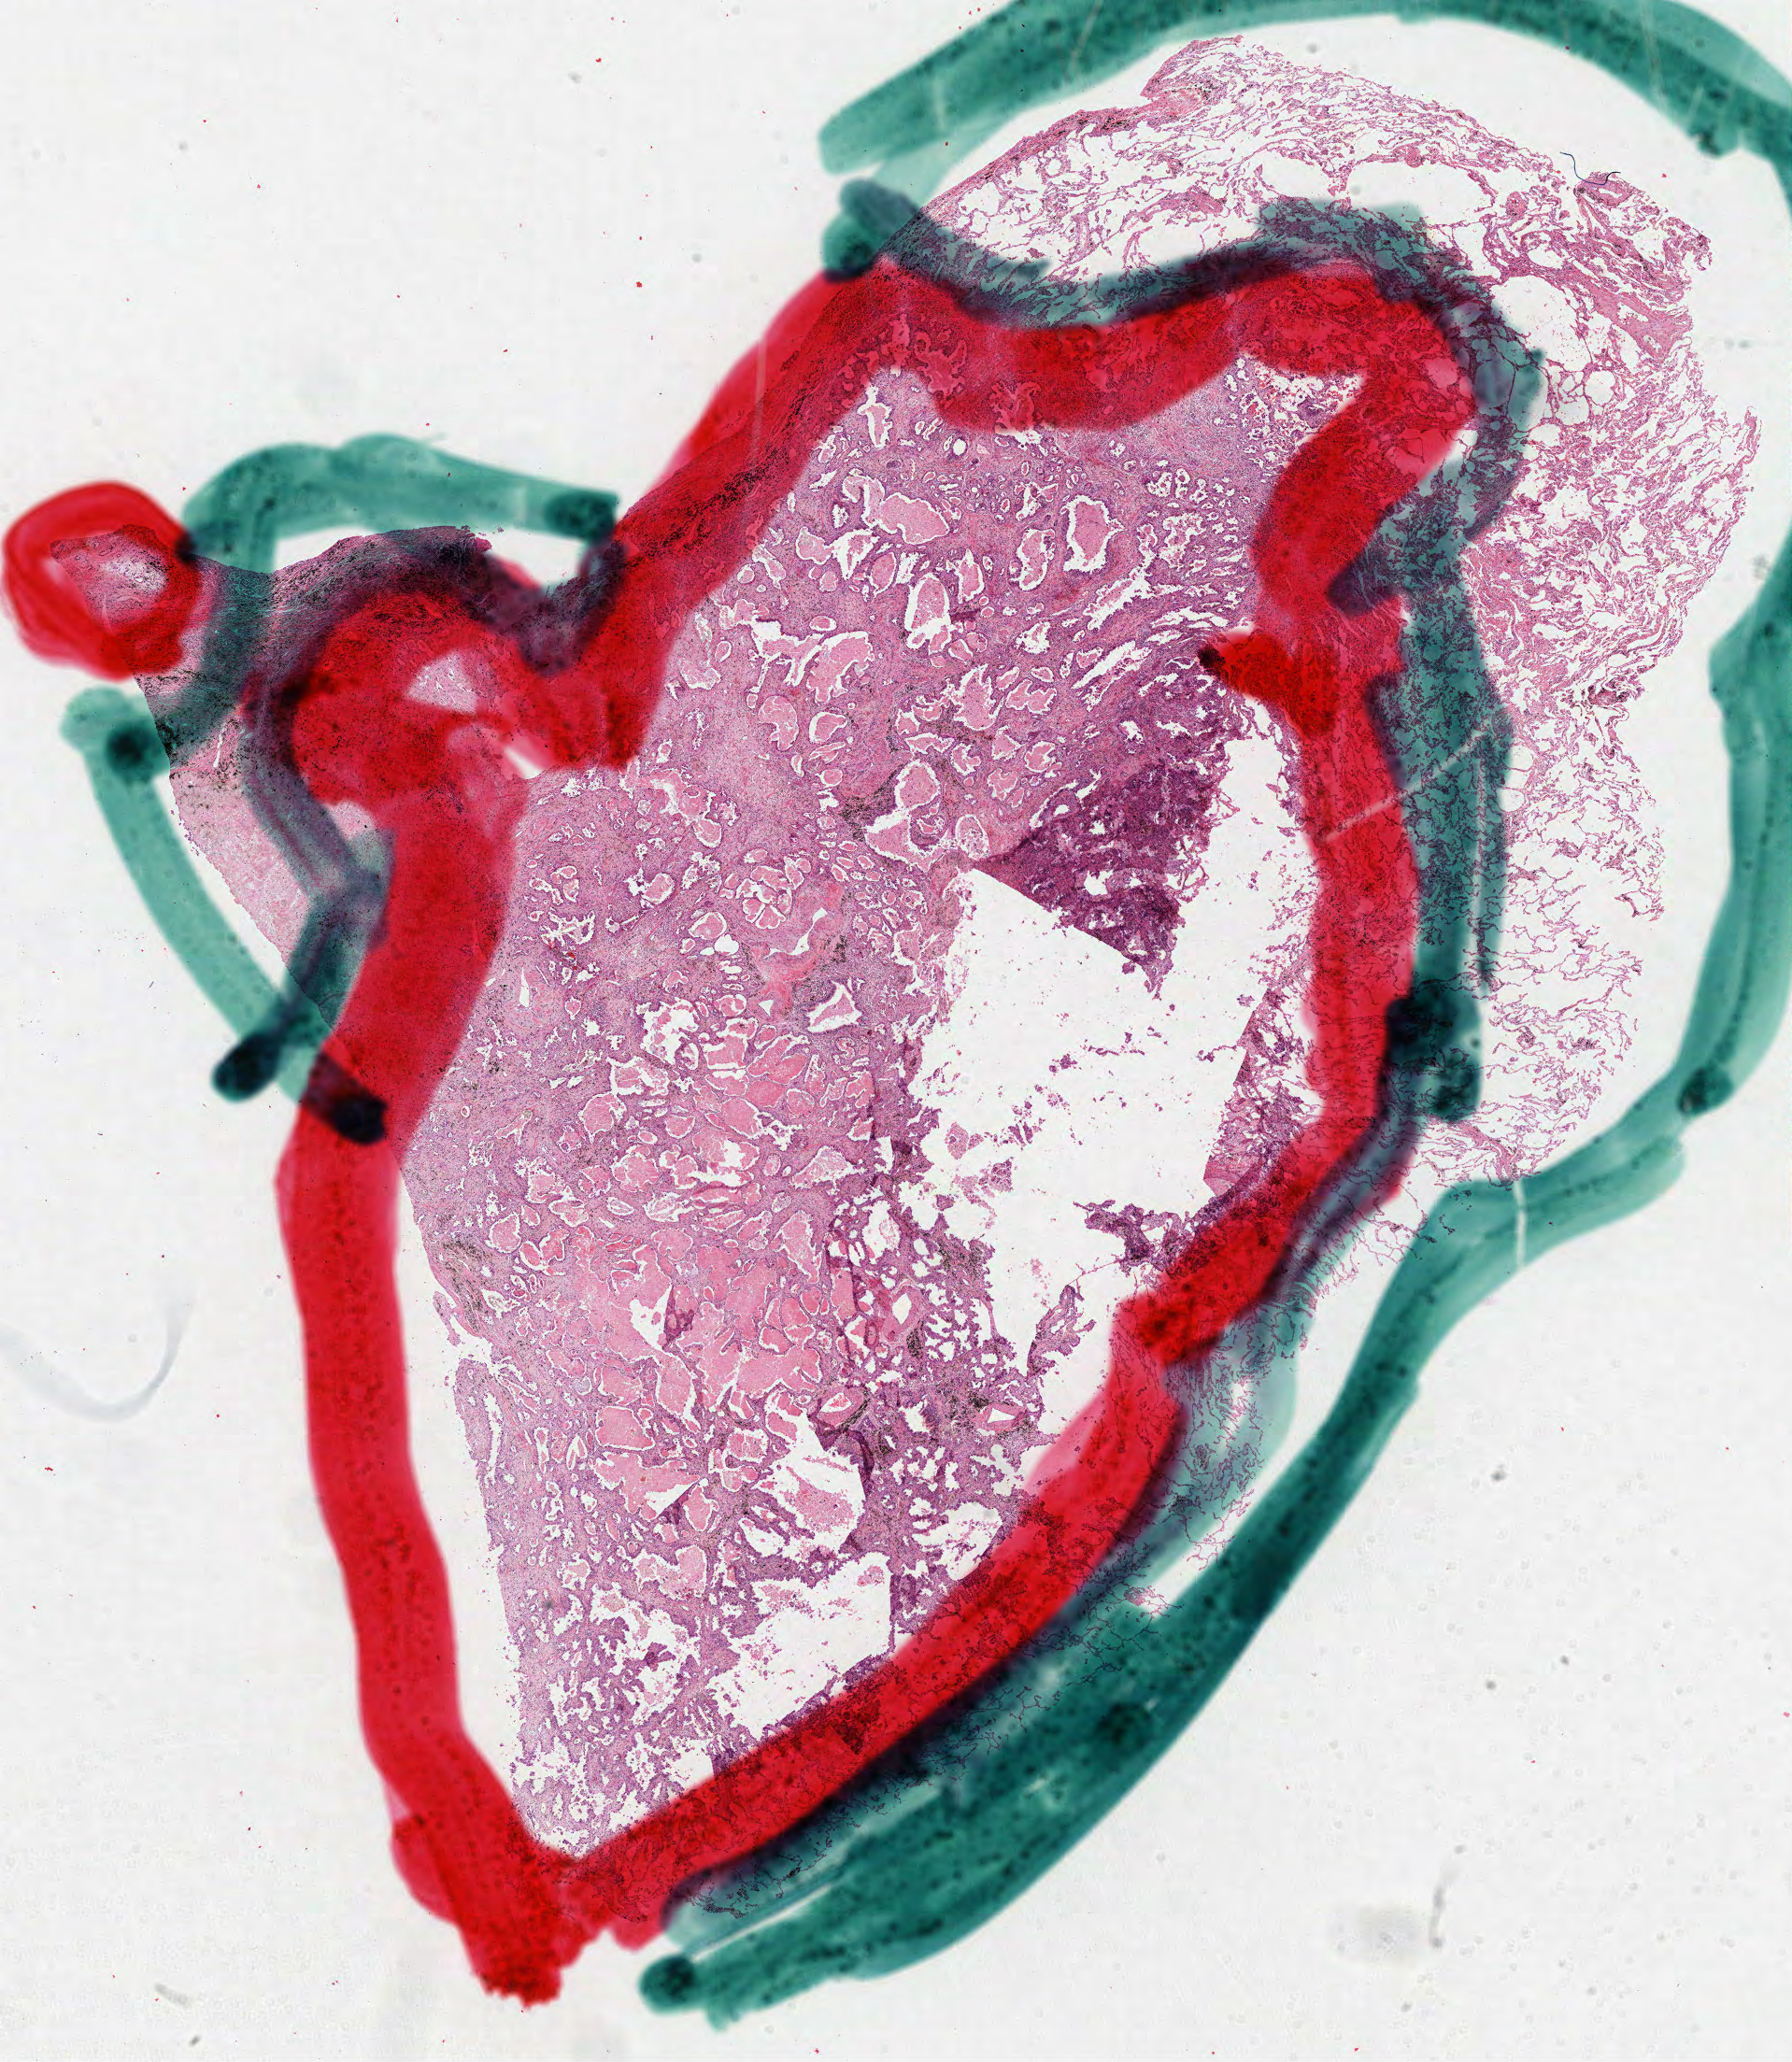
Hematoxylin and eosin (H&E) stained whole-slide image, shown as a low-resolution overview of the whole scanned area (about 15.5 x 17.8 mm, slide scanned at 40x); formalin-fixed paraffin-embedded (FFPE) diagnostic section; sample: primary tumour, lung. Patient: male, age at initial diagnosis 58 years.
- laterality: left
- AJCC pathologic stage: IB (7th edition)
- diagnosis: Bronchiolo-alveolar adenocarcinoma, NOS (upper lobe, lung)